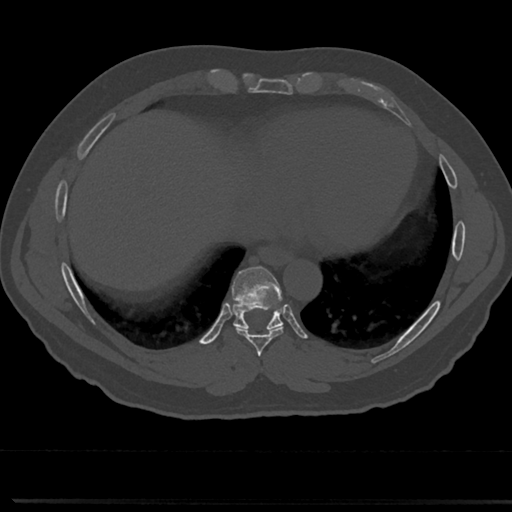
CT including the spine, one axial slice. Slice 333 of 817 in the series (ordered by position). Bone window (W 1800 / L 400 HU). 0.5 mm slice thickness. 512 × 512 image matrix, field of view 355 × 355 mm. Male patient, age 61 years. From the clinical record (not read from this slice): primary cancer: prostate.
Outlined on this slice (semi-automatically segmented with operator editing):
- T7 vertebra: box from (x=259, y=347) to (x=266, y=377) px
- T8 vertebra: (x=210, y=271)–(x=309, y=356)